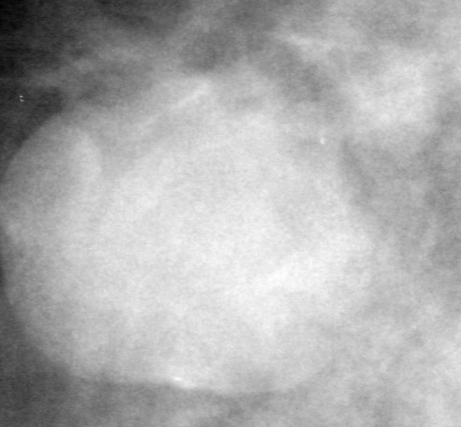
Region of interest cut from a scanned film mammogram (one marked finding), right breast, MLO view.
Marked abnormality: mass, shape round, margins spiculated; BI-RADS assessment category 3; pathology (as recorded): malignant.